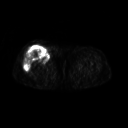
FDG PET of an extremity soft-tissue mass (from a PET/CT study), one axial slice; position 242 of 311 along the scan axis; 128 × 128 image matrix, field of view 500 × 500 mm. Patient: female, 57 years. Case-level facts recorded for this patient, not image findings: histological type: pleiomorphic undifferentiated sarcoma; grade: high; site of the primary tumour: right quadricep.
Outlined on this slice (expert contour drawn on MRI and transferred to this co-registered scan by the dataset authors):
- tumour plus oedema (research contour): box from (x=24, y=47) to (x=49, y=71) px
- tumour (research contour): (x=24, y=47)–(x=49, y=71)